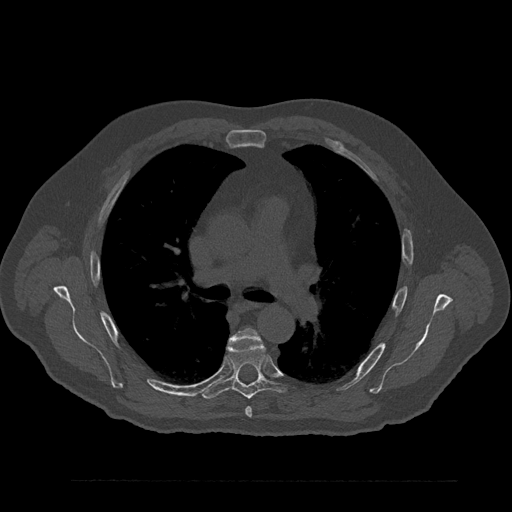
CT including the spine, one axial slice; position 566 of 797 along the scan axis; reconstruction kernel Br40s/3; bone window (W 1800 / L 400 HU); 512 × 512 image matrix, field of view 430 × 430 mm. Male patient, age 61 years. From the clinical record (not read from this slice): primary cancer: prostate.
Annotated regions visible in this slice (semi-automatically segmented with operator editing):
- T5 vertebra: bounding box <230,328,260,418> (left, top, right, bottom; pixels)
- T6 vertebra: <202,342,287,399>